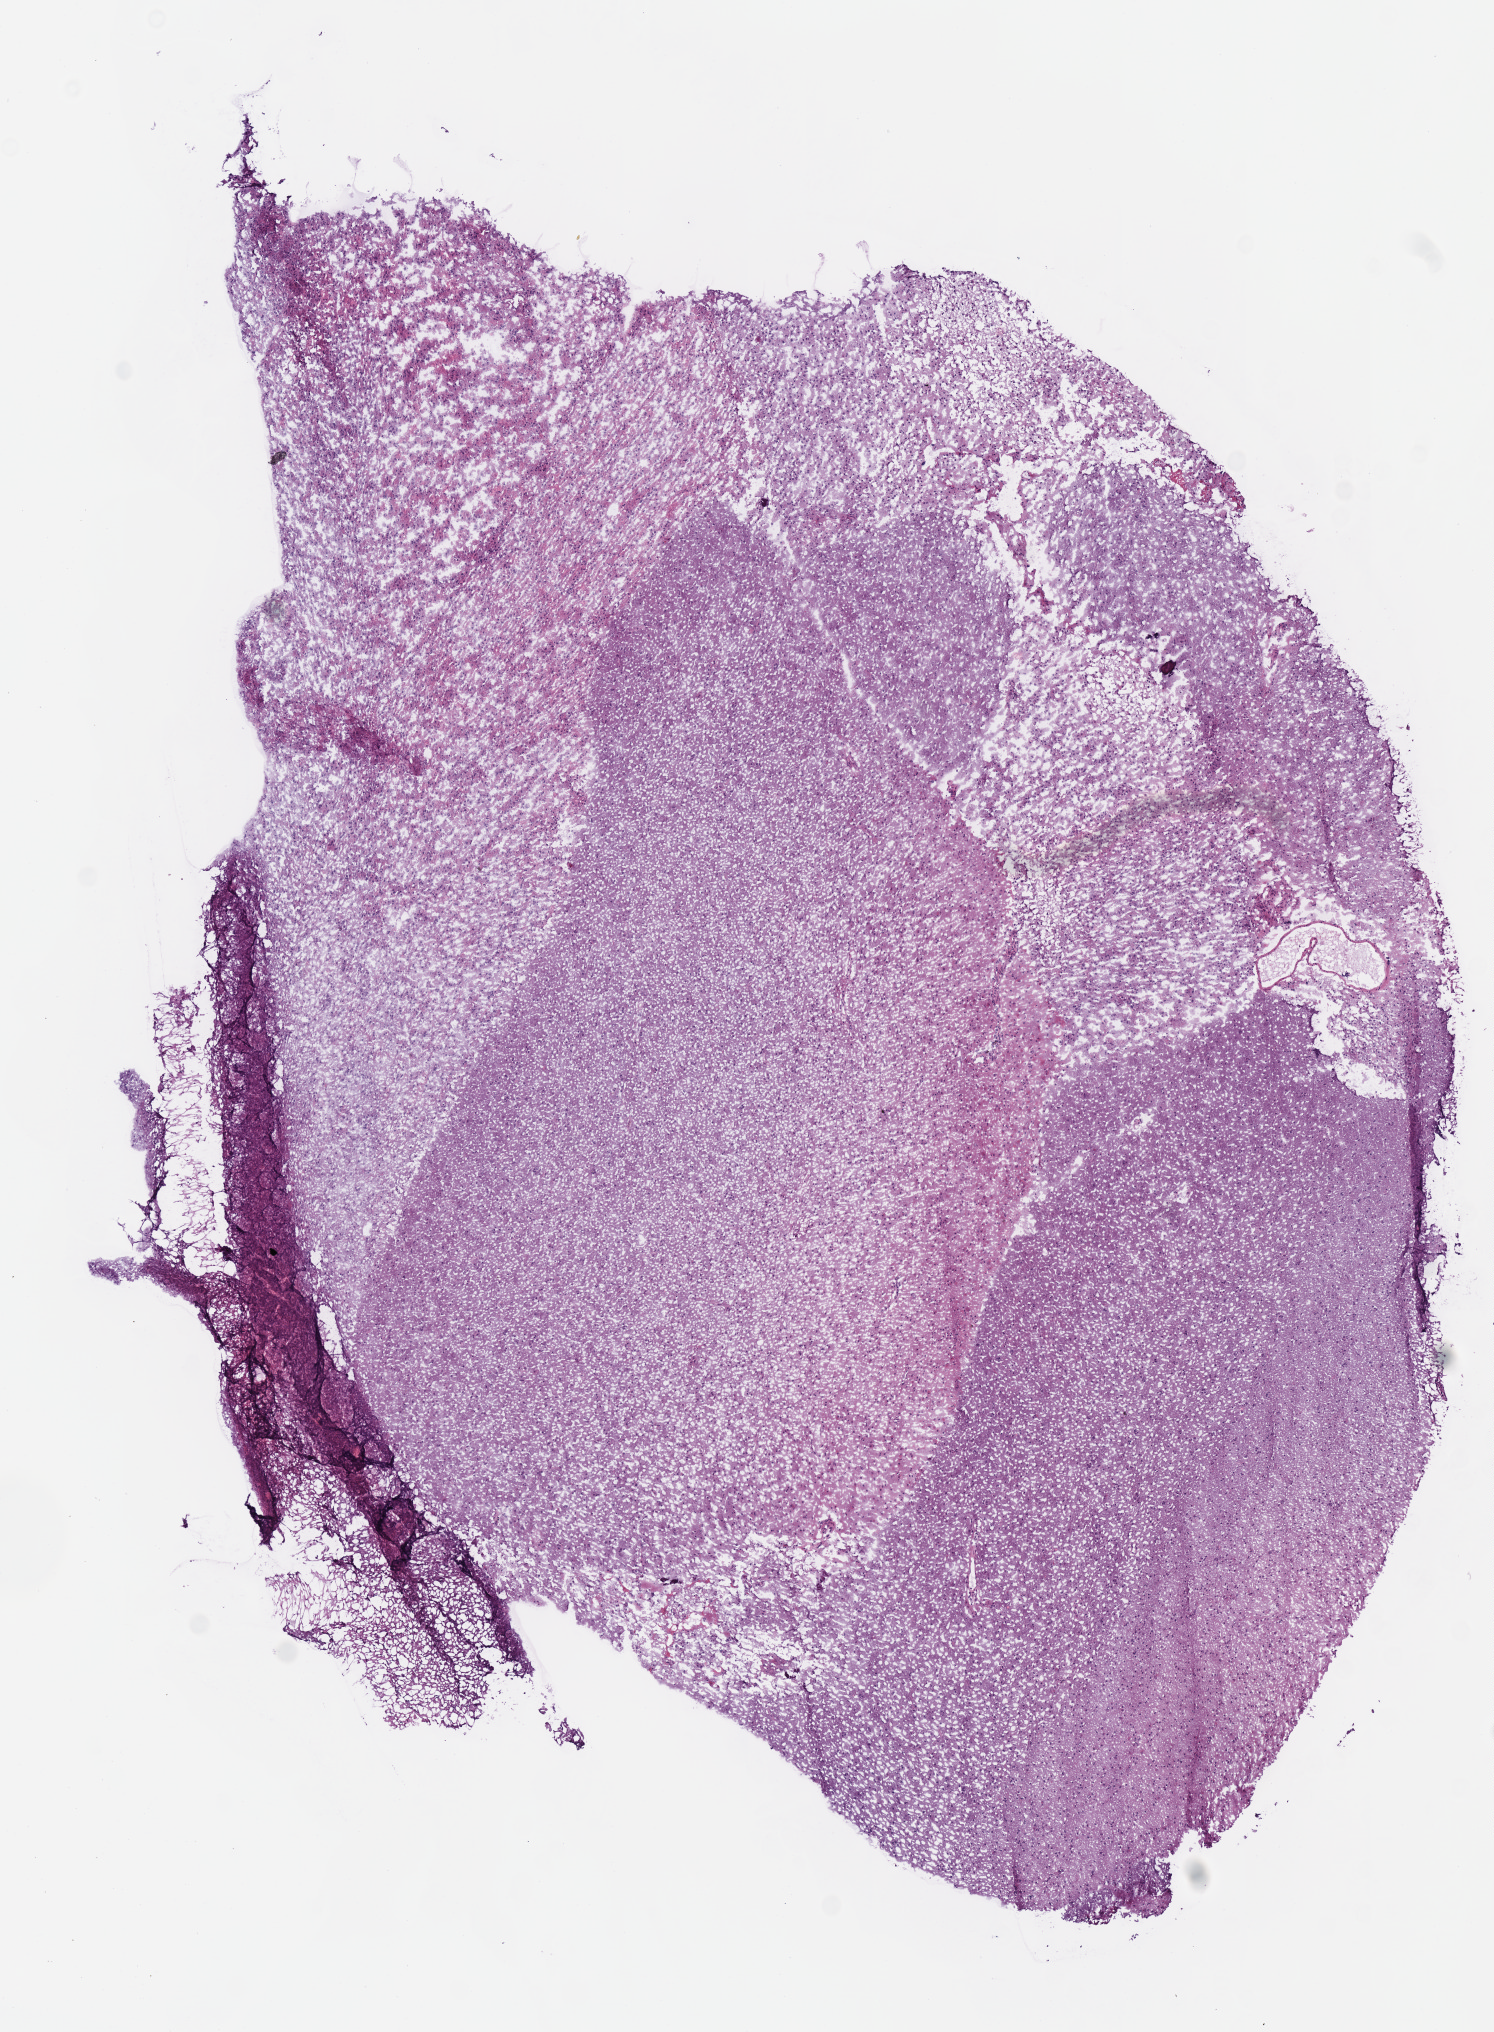
Digitized H&E-stained tissue section (whole slide) — a low-resolution overview of the entire scanned area, about 5.9 x 8.0 mm, frozen section from the top of the tissue portion, sample: primary tumour, brain. Patient: female, age at initial diagnosis 29 years. Histologic grade: G2 (moderately differentiated). Composition of this section per pathologist review: tumour cells 100%, tumour nuclei 70%, normal cells 0%, stromal cells 0%, necrosis 0%.
Diagnosis: Mixed glioma (cerebrum).